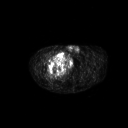
FDG PET of an extremity soft-tissue mass (from a PET/CT study), one axial slice. Slice 279 of 311 in the series (ordered by position). 3.27 mm slice thickness. 128 × 128 image matrix. Male patient, age 50 years. Case-level facts recorded for this patient, not image findings: histological type: undifferentiated - pleiomorphic; grade: high; site of the primary tumour: right thigh.
Annotated regions visible in this slice (expert contour drawn on MRI and transferred to this co-registered scan by the dataset authors):
- gross tumour volume including surrounding oedema: bounding box (x1, y1, x2, y2) in pixels: (49, 51, 66, 68)
- gross tumour volume (mass): (49, 51, 65, 68)